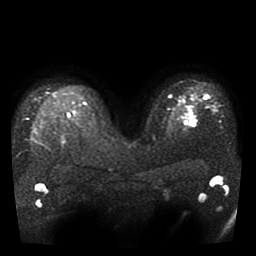
Breast MRI, one axial slice. Slice 29 of 41 in the series (ordered by position). Diffusion-weighted series; image 2 of 4 stored at this slice position (different b-values; order by instance number). 1.5 T. 256 × 256 image matrix, field of view 330 × 330 mm. Female patient.
Structures marked on this image (manually delineated by an expert):
- tumour on diffusion-weighted imaging: bounding box (x1, y1, x2, y2) in pixels: (191, 119, 195, 126)